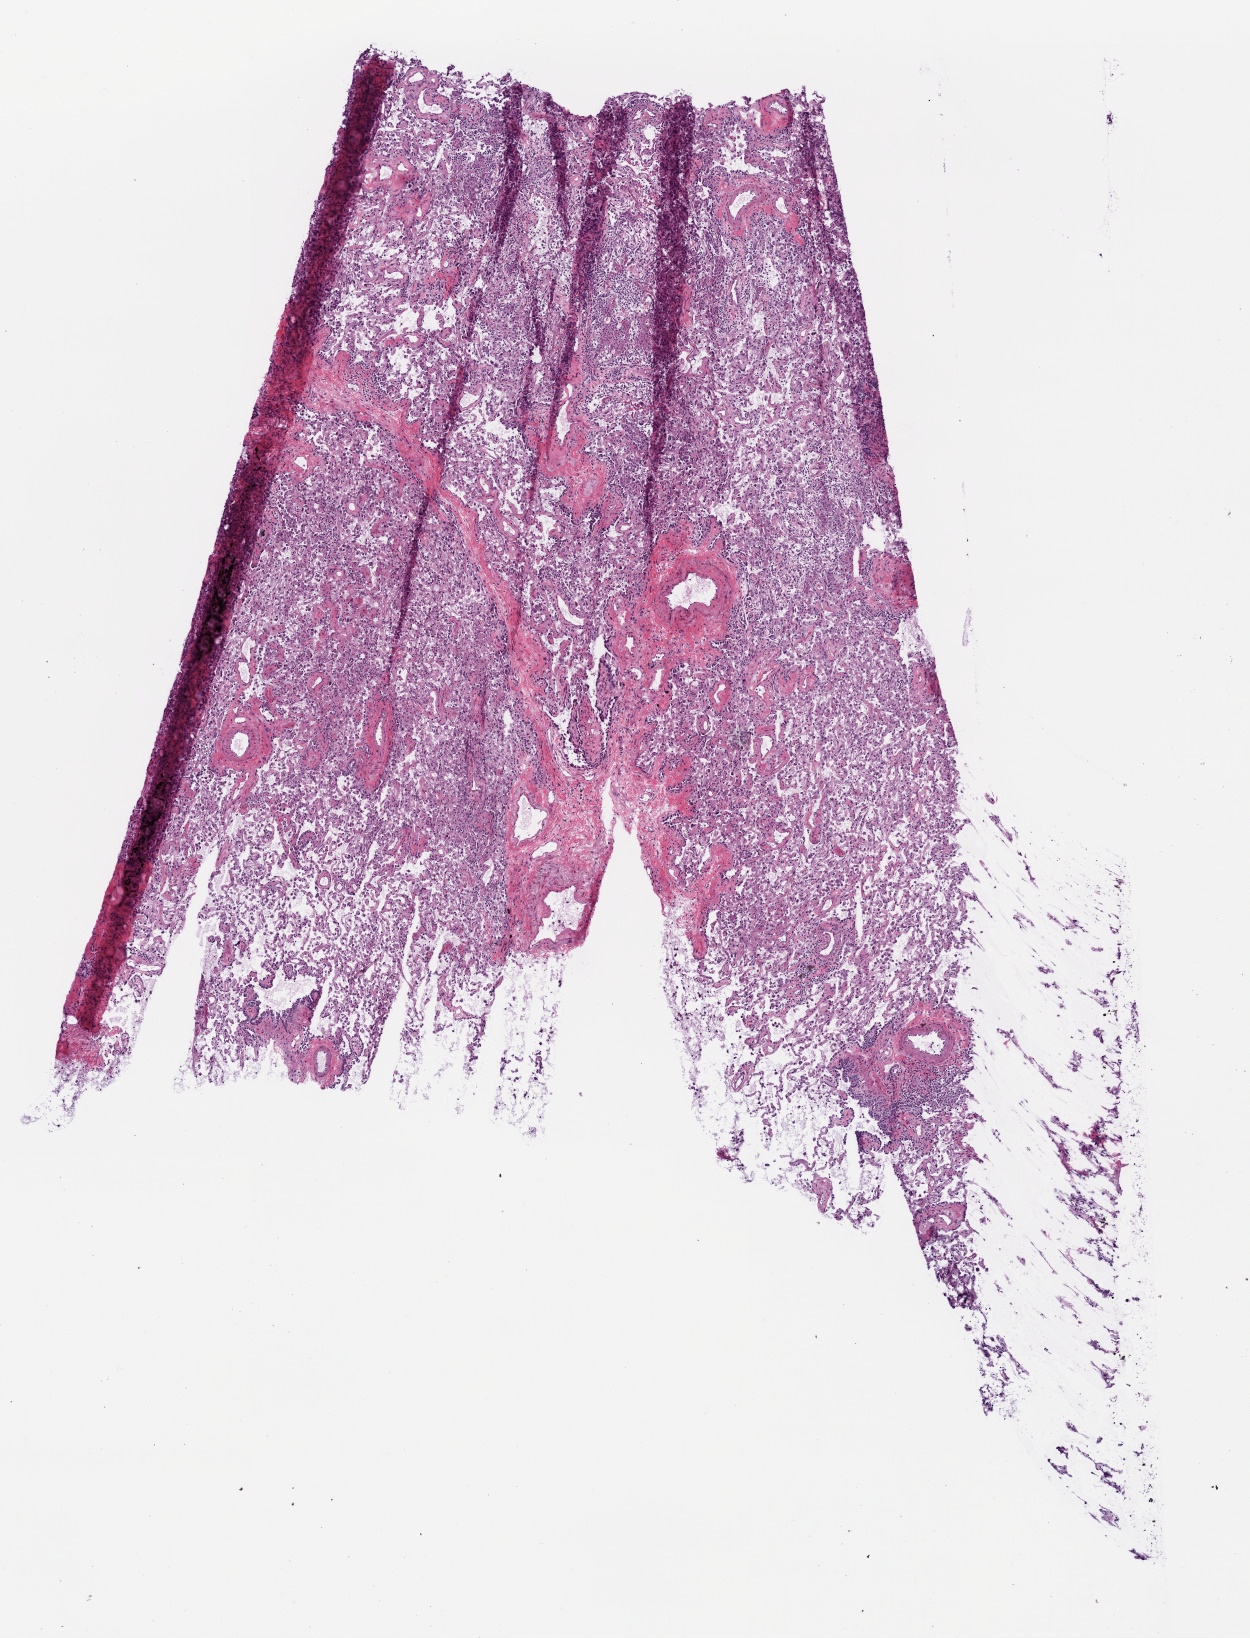
Hematoxylin and eosin (H&E) stained whole-slide image — a low-resolution overview of the entire scanned area, about 5.0 x 6.6 mm, frozen section, solid tissue normal (non-tumour tissue) sample from the lung. Male, age 65 years at initial diagnosis.
This section: solid tissue normal (non-tumour) sample from the same patient. Patient diagnosis: Basaloid squamous cell carcinoma (upper lobe, lung).